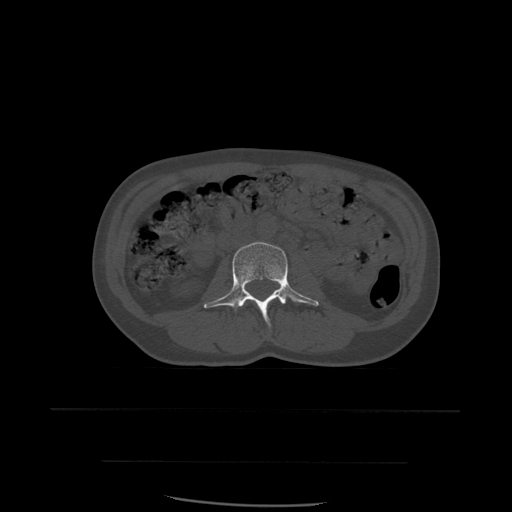
CT including the spine, one axial slice; position 200 of 574 along the scan axis; bone window (W 1800 / L 400 HU); 1.25 mm slice thickness; 512 × 512 image matrix. Patient age 48 years. From the clinical record (not read from this slice): primary cancer: lung.
Structures marked on this image (semi-automatic segmentation, software-assisted and operator-edited):
- L3 vertebra: bounding box <204,242,319,326> (left, top, right, bottom; pixels)